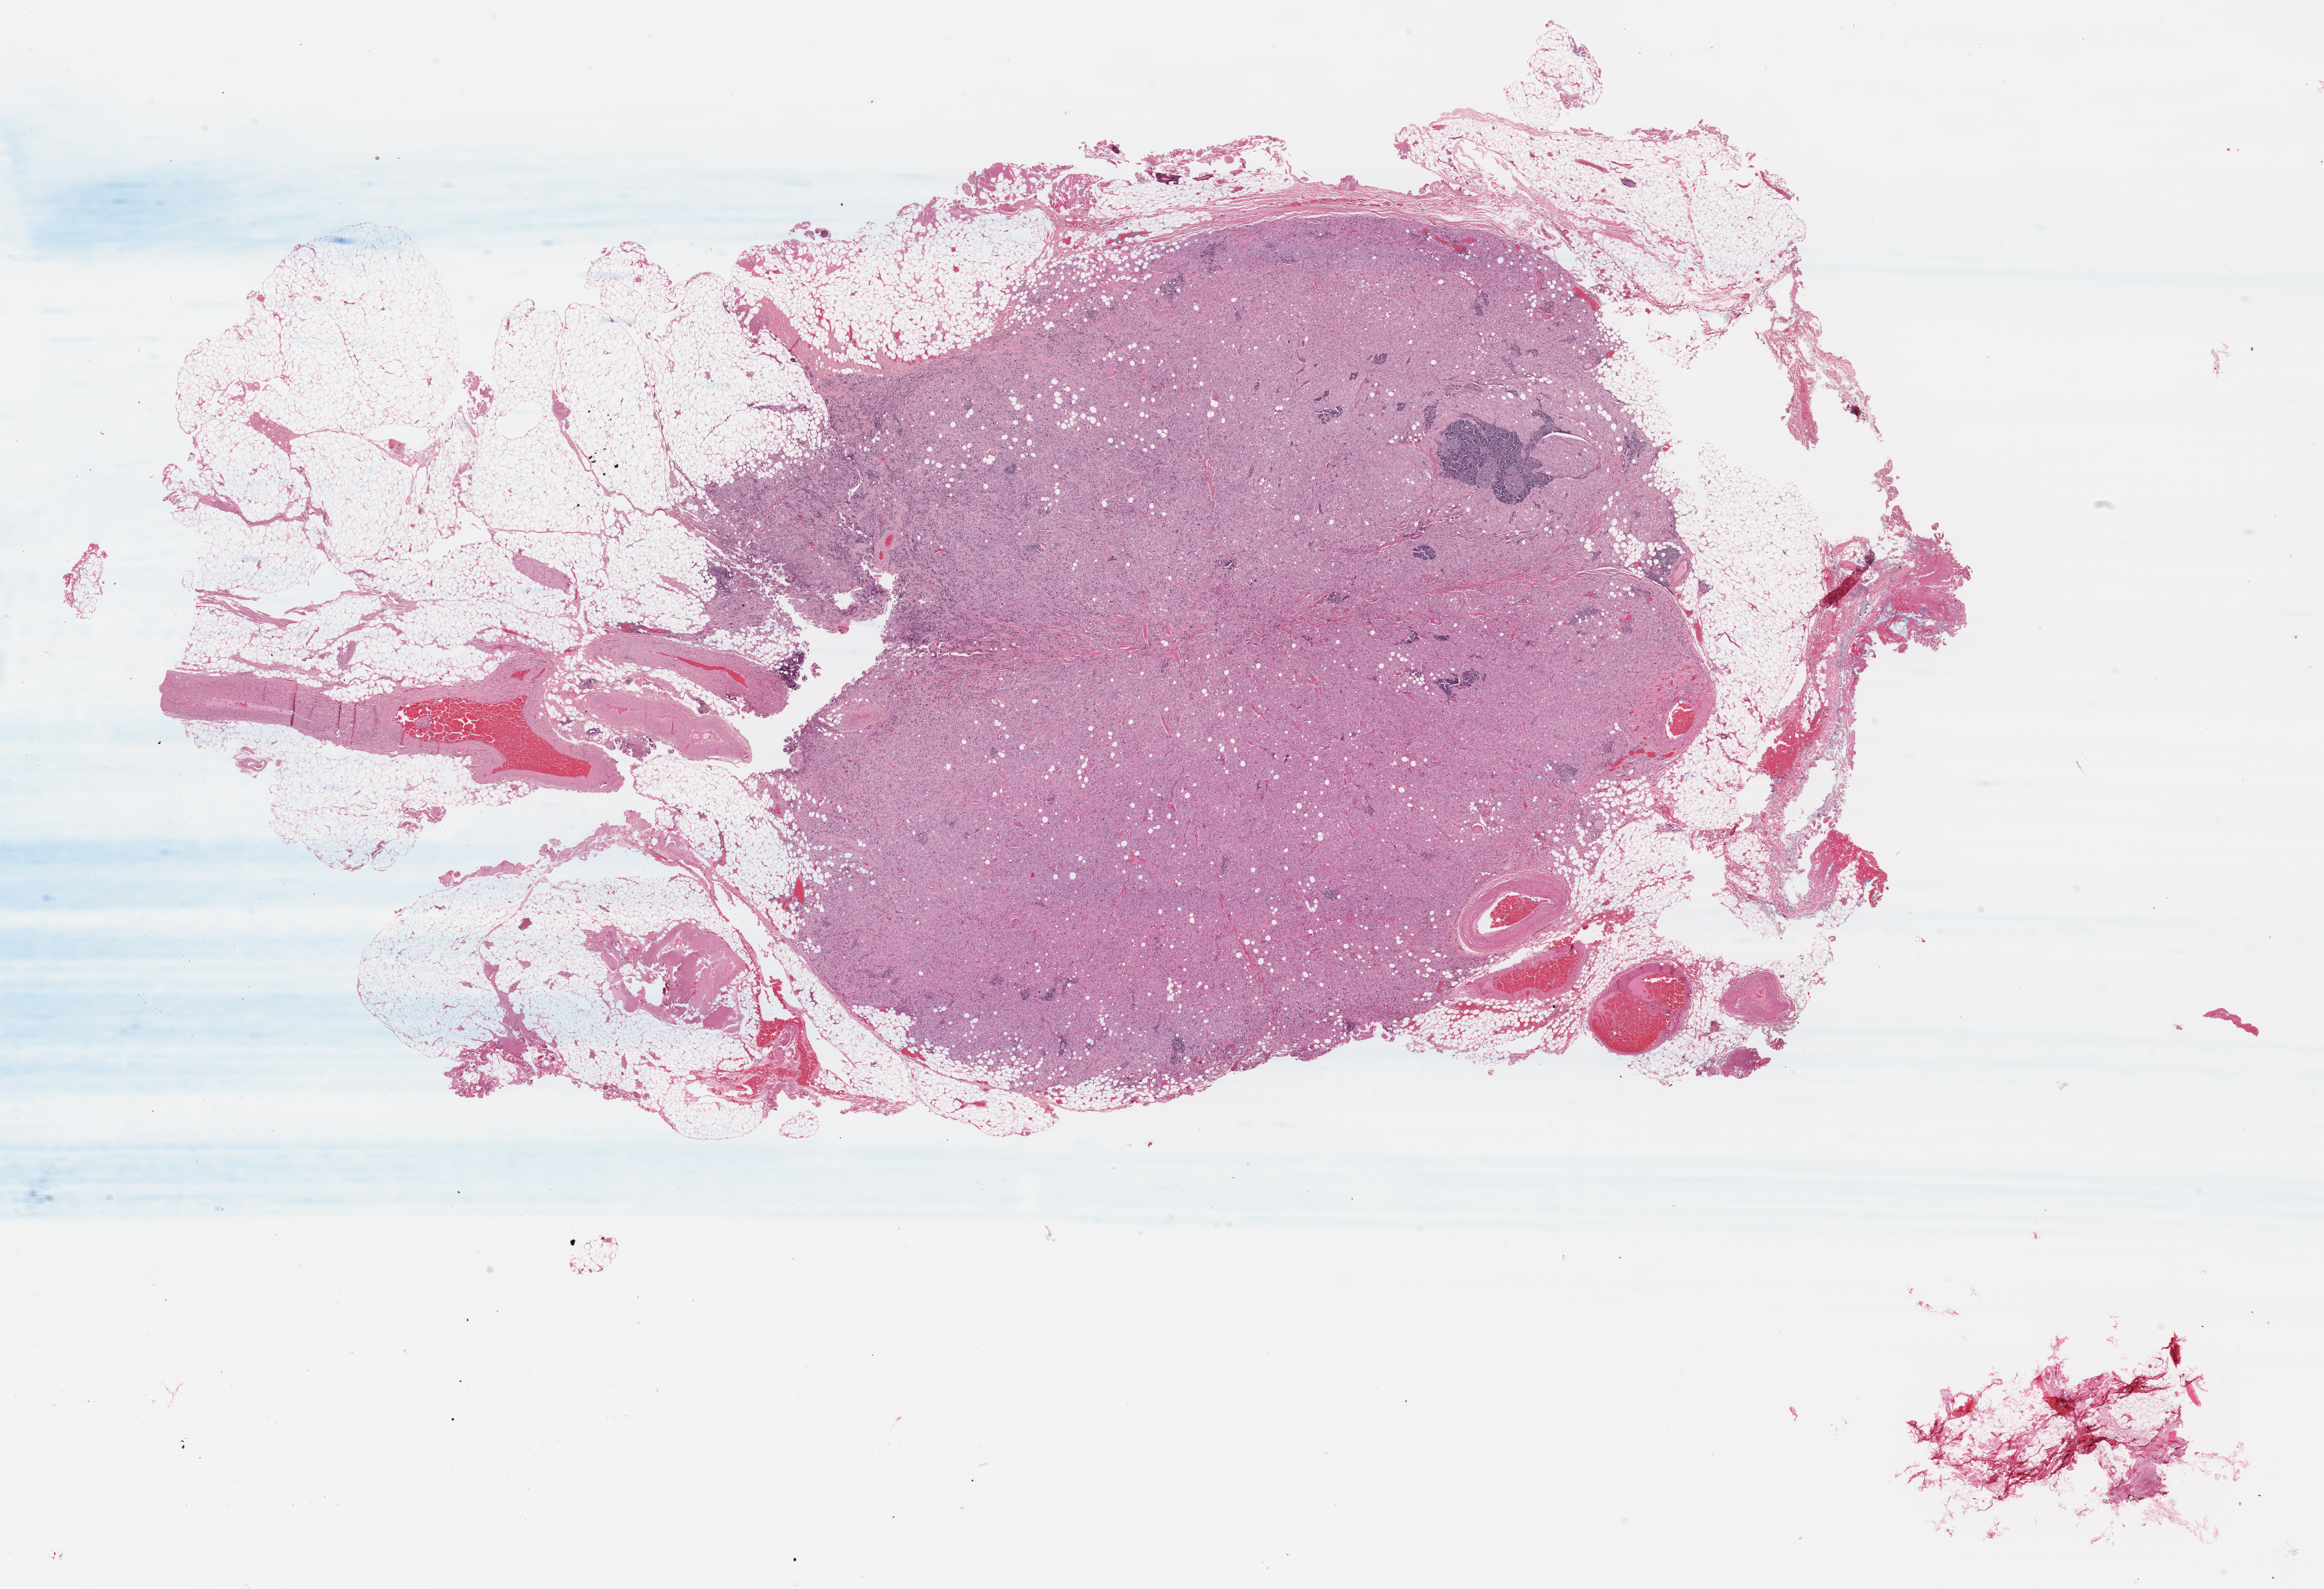
Whole-slide histology image, H&E — shown as a low-resolution overview of the whole scanned area (about 27.4 x 18.7 mm, acquisition: 40x scan), FFPE section, primary tumour sample from the skin. Female, age 70 years at initial diagnosis.
- diagnosis: Malignant melanoma, NOS